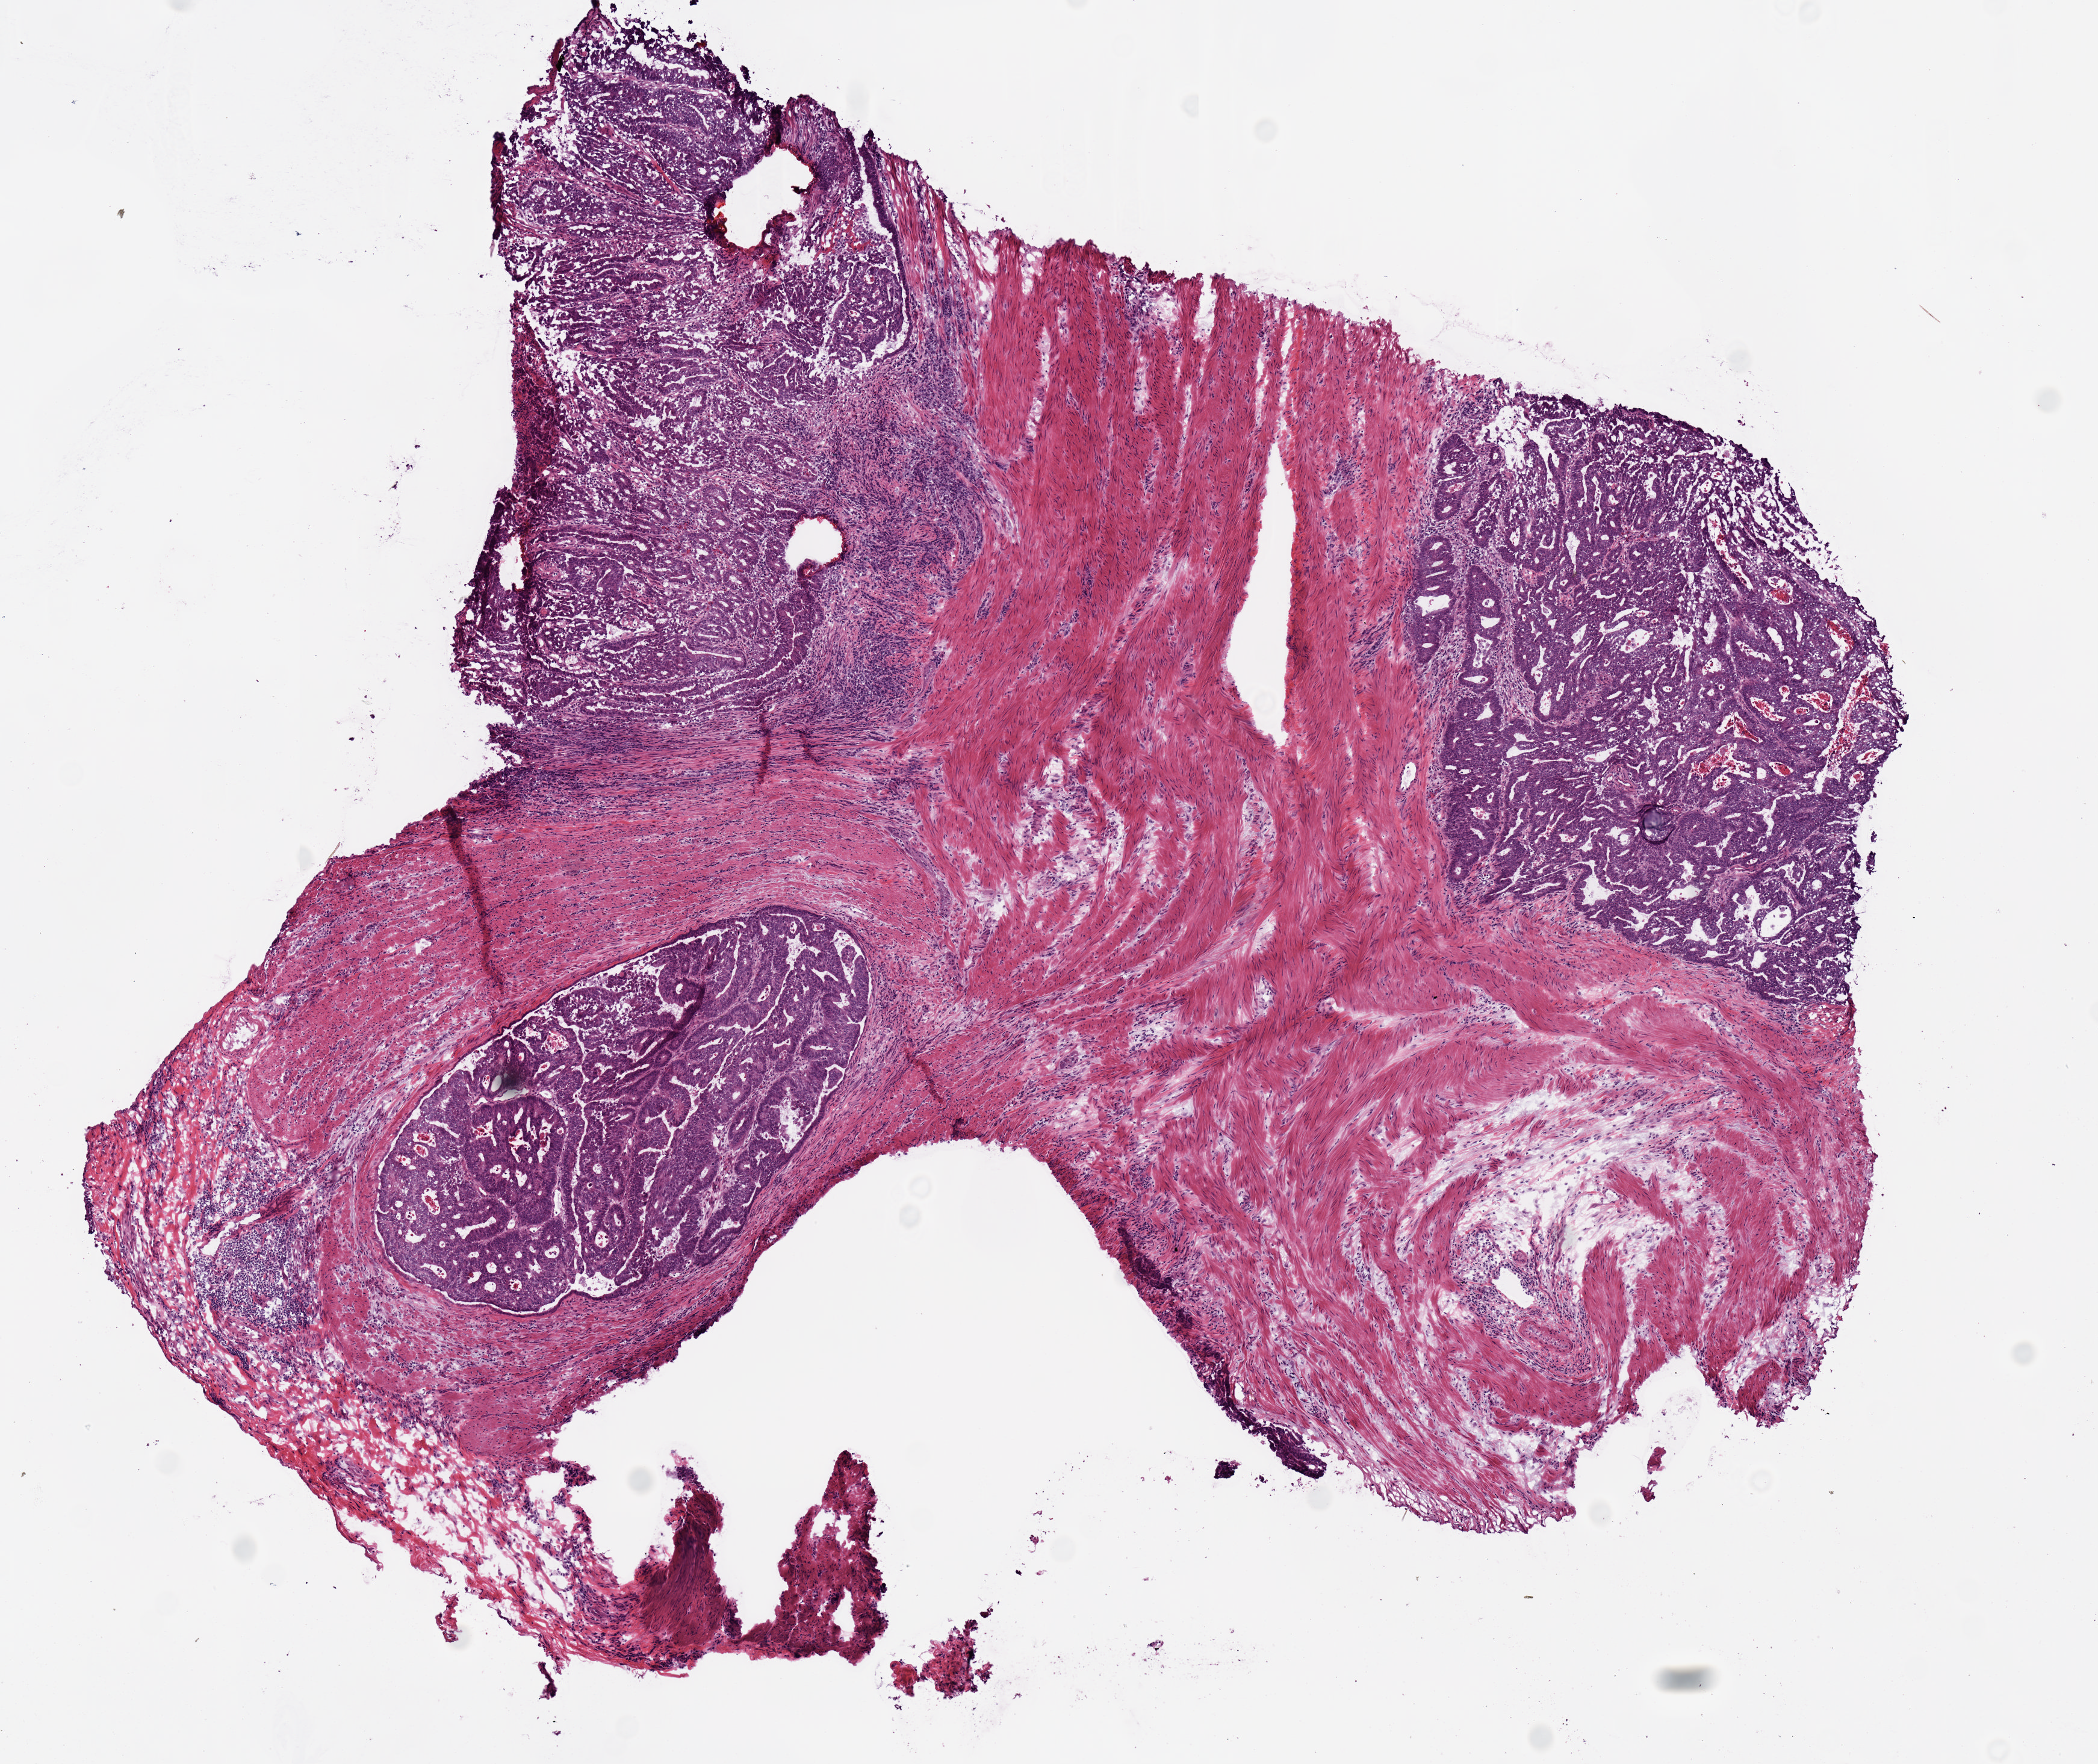
Digitized H&E tissue section (whole slide), whole scanned area (about 6.9 x 5.8 mm) shown as a low-resolution overview; frozen section from the bottom of the tissue portion; rectum, primary tumour sample. Patient: male, age at initial diagnosis 63 years. Pathologist review of this section (percent, as recorded): tumour cells 55%, tumour nuclei 80%, normal cells 0%, stromal cells 25%, necrosis 20%.
- lymph nodes positive (case pathology): 0 of 16 examined
- AJCC pathologic stage: IIC (7th edition)
- histologic diagnosis: Tubular adenocarcinoma